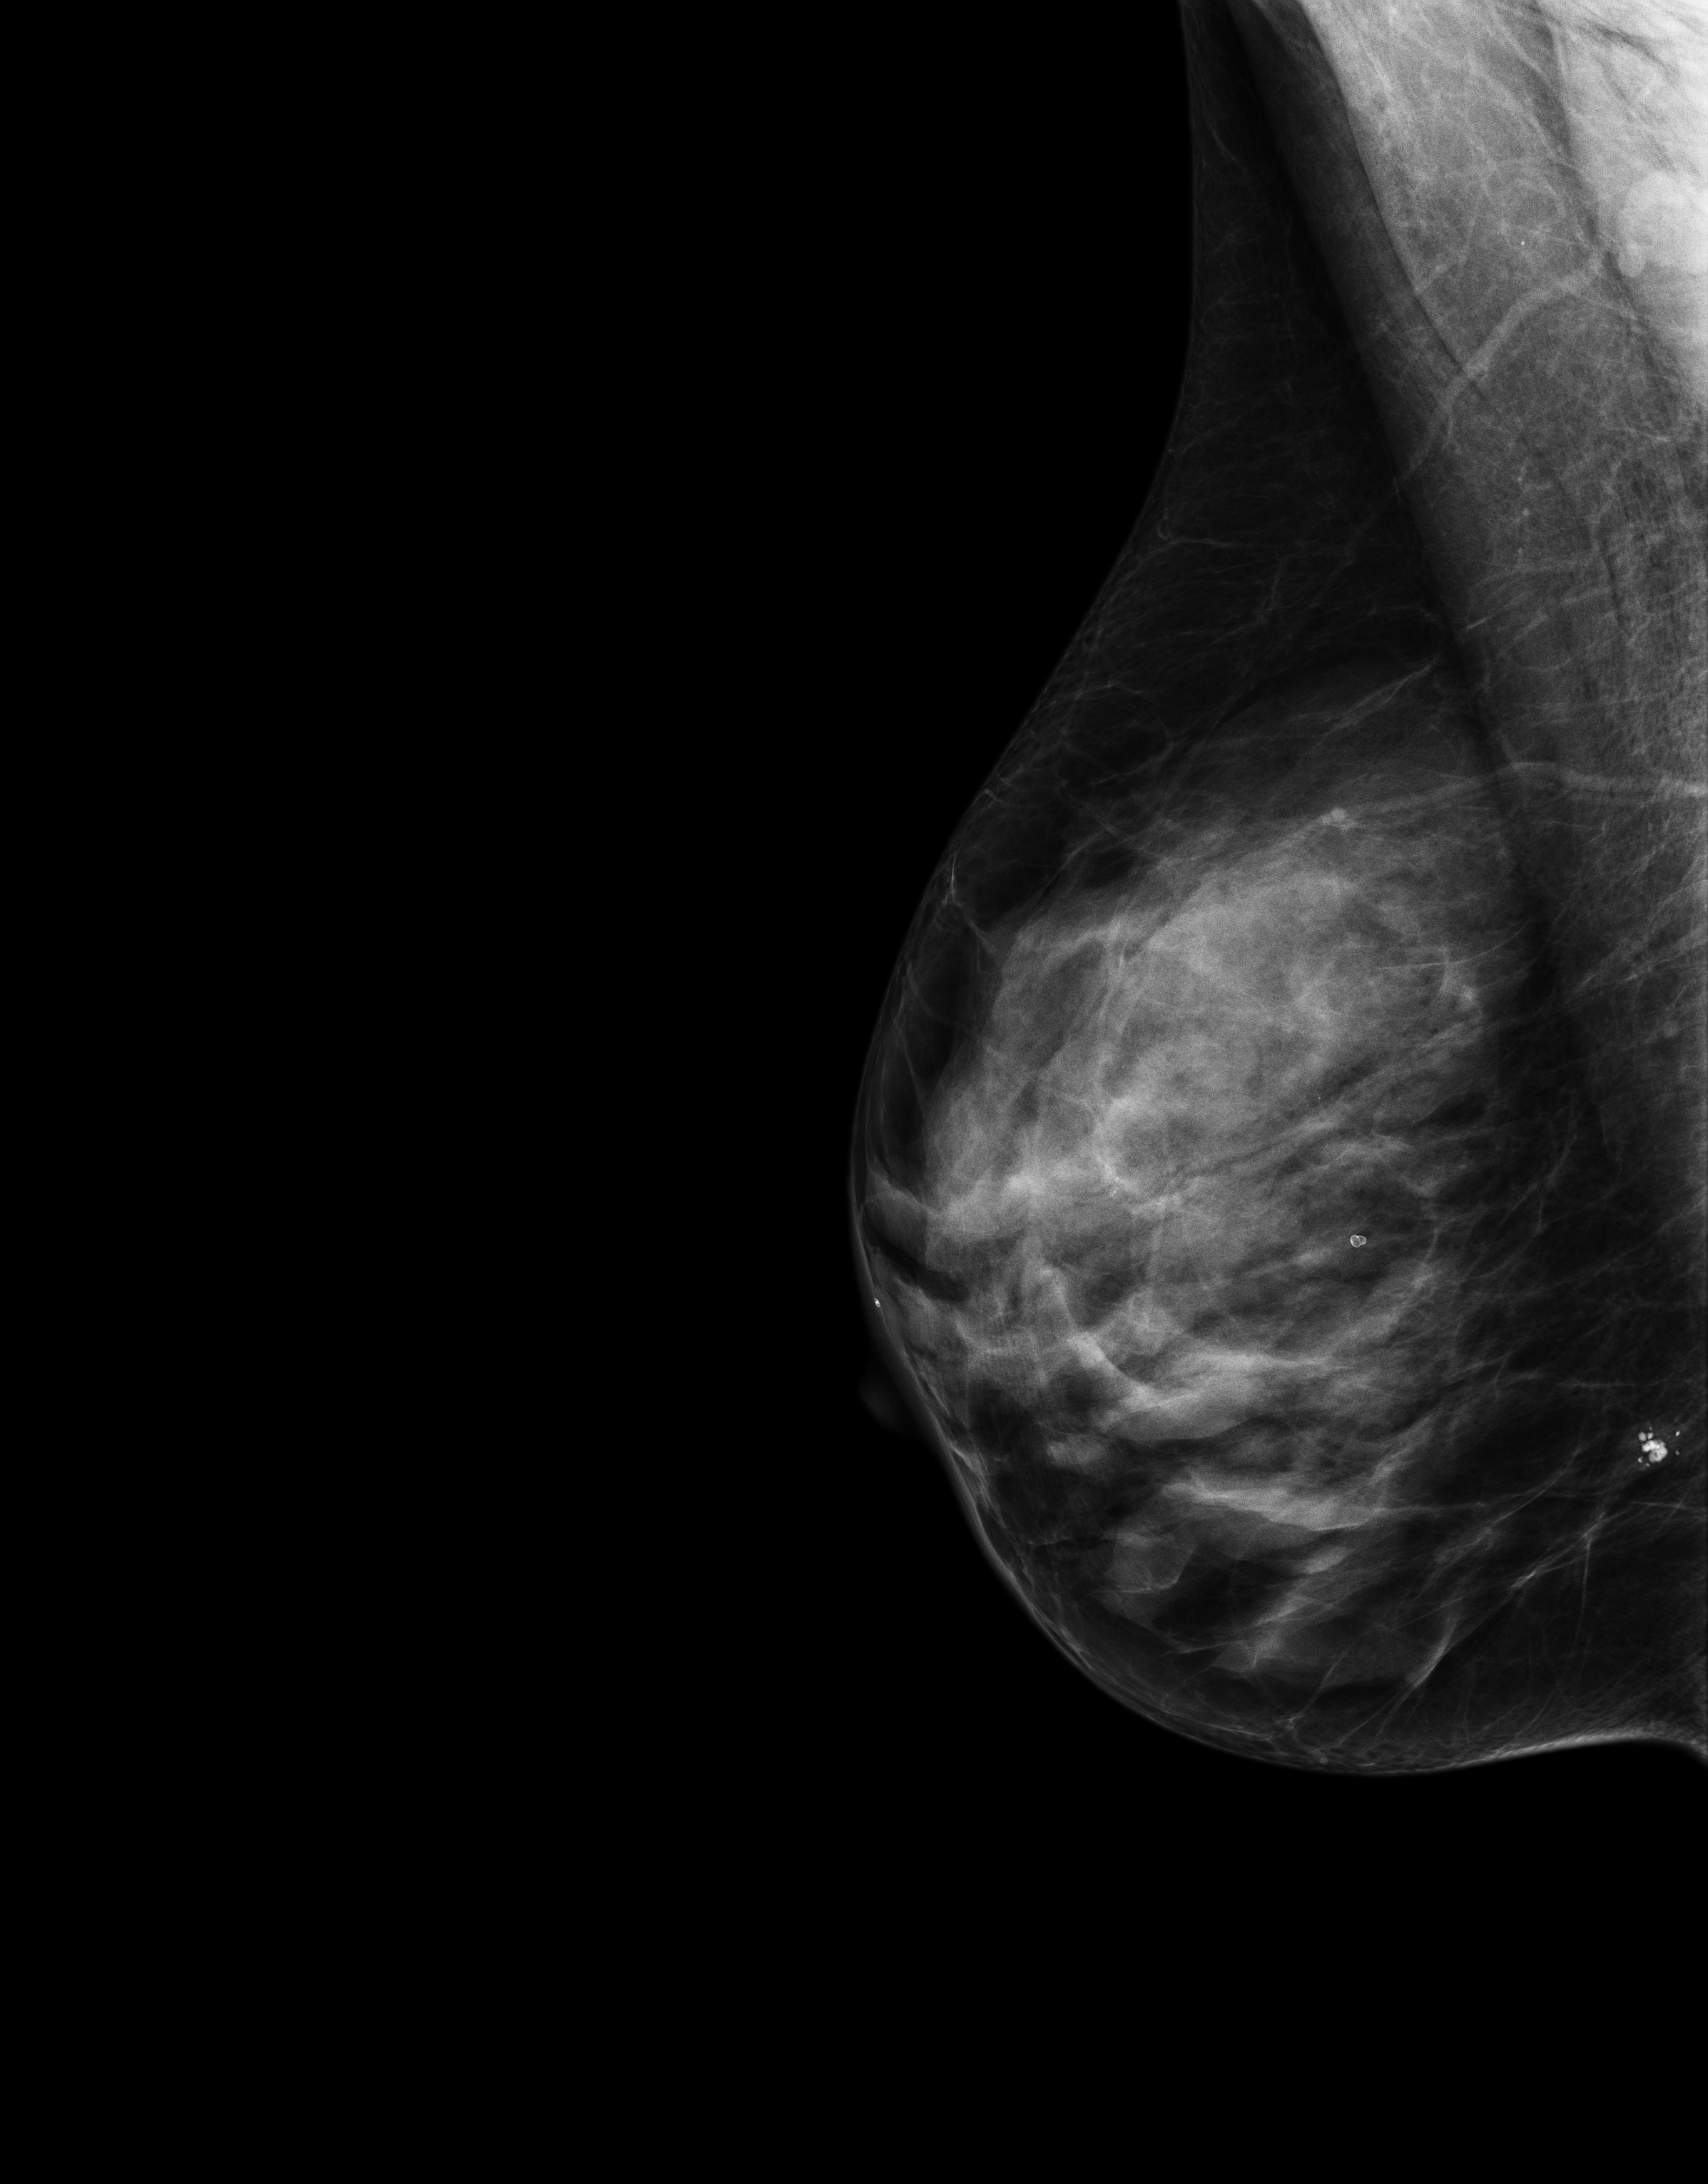
Digital mammogram (FFDM); right breast; medio-lateral oblique projection; annual screening mammography examination. Female patient, age 60 years.
Breast density at the screening exam (both breasts): extremely dense (BI-RADS density category d). Final BI-RADS assessment for this screening round (tomosynthesis exam, both breasts): category 1. Recall: no recall after this screen.